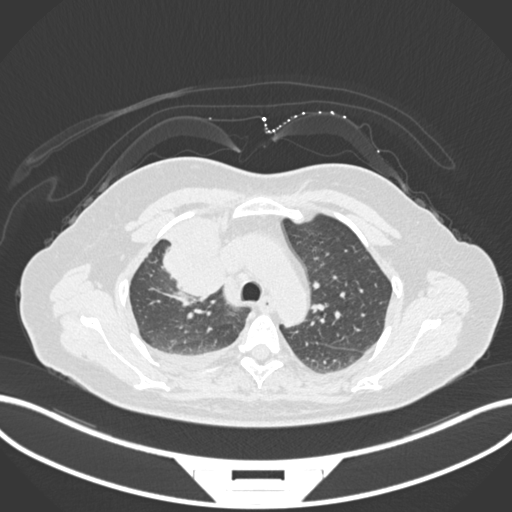
Chest CT, one axial slice; slice 114 of 172 in the series (ordered by position); lung window (W 1500 / L -600 HU); 512 × 512 image matrix. Patient: female, 52 years. From the clinical record (not read from this slice): clinical TNM (as recorded): T3 N1 M1.
Outlined on this slice (bounding box drawn by a radiologist):
- lung tumour (recorded histology: adenocarcinoma): bounding box (x1, y1, x2, y2) in pixels: (158, 207, 232, 302)